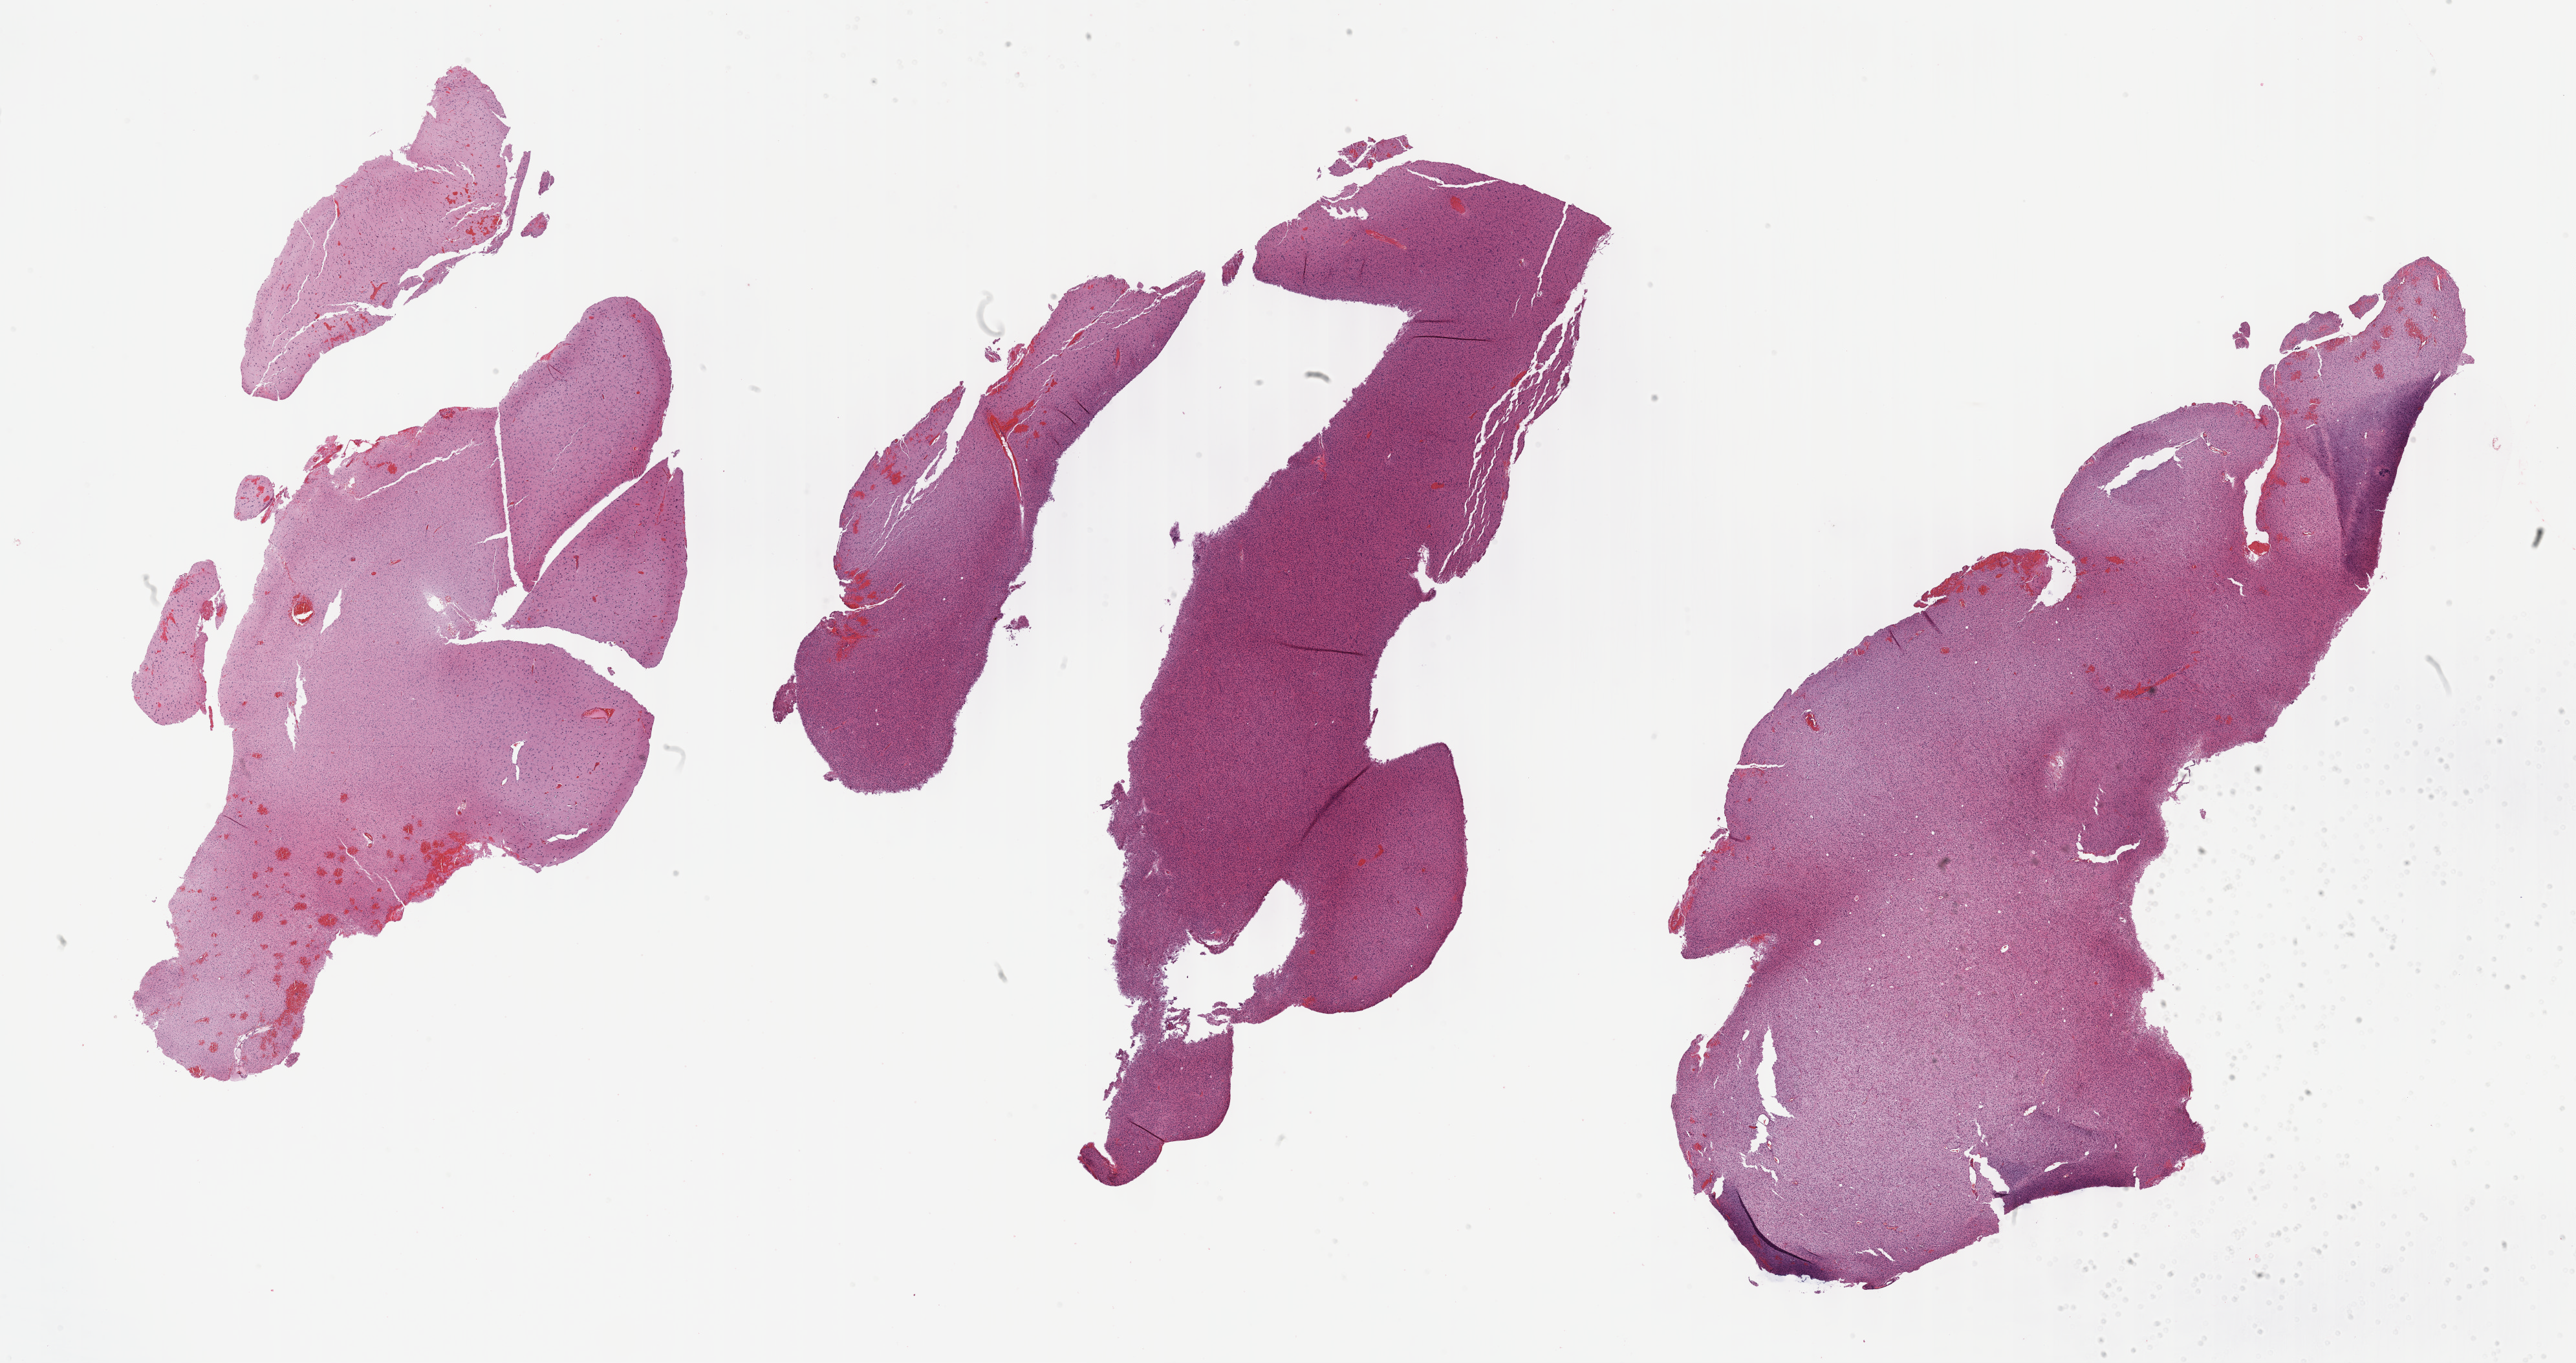
Whole-slide histology image, H&E — shown as a low-resolution overview of the whole scanned area (about 32.2 x 17.0 mm, from a 40x scan). Formalin-fixed paraffin-embedded (FFPE) diagnostic section. Primary tumour sample from the brain. Patient: male, age at initial diagnosis 25 years. Histologic grade: G2 (moderately differentiated).
Pathologic diagnosis: Oligodendroglioma, NOS (cerebrum). Laterality: left.